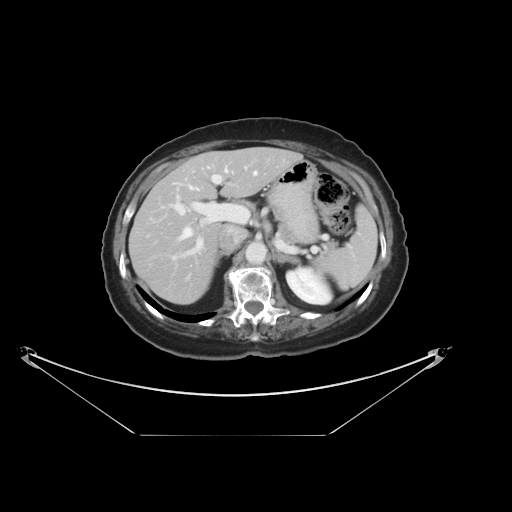
Contrast-enhanced abdominal CT, one axial slice; position 22 of 36 along the scan axis; reconstruction kernel STANDARD; 120 kVp; intravenous contrast given; soft-tissue window (W 400 / L 40 HU); 5 mm slice thickness; 512 × 512 image matrix, field of view 500 × 500 mm. Female patient, age 70 years. From the clinical record (not read from this slice): diagnosis: colorectal cancer liver metastases, imaged before liver resection; multiple liver metastases: no; largest metastasis: 2.5 cm; disease in both lobes: no.
Annotated regions visible in this slice (outlined manually by an expert reader):
- hepatic veins: bounding box (x1, y1, x2, y2) in pixels: (145, 167, 257, 245)
- liver: (131, 149, 300, 304)
- planned liver remnant (the part of the liver to remain after resection): (131, 149, 300, 304)
- portal vein (with intrahepatic branches): (161, 167, 247, 279)